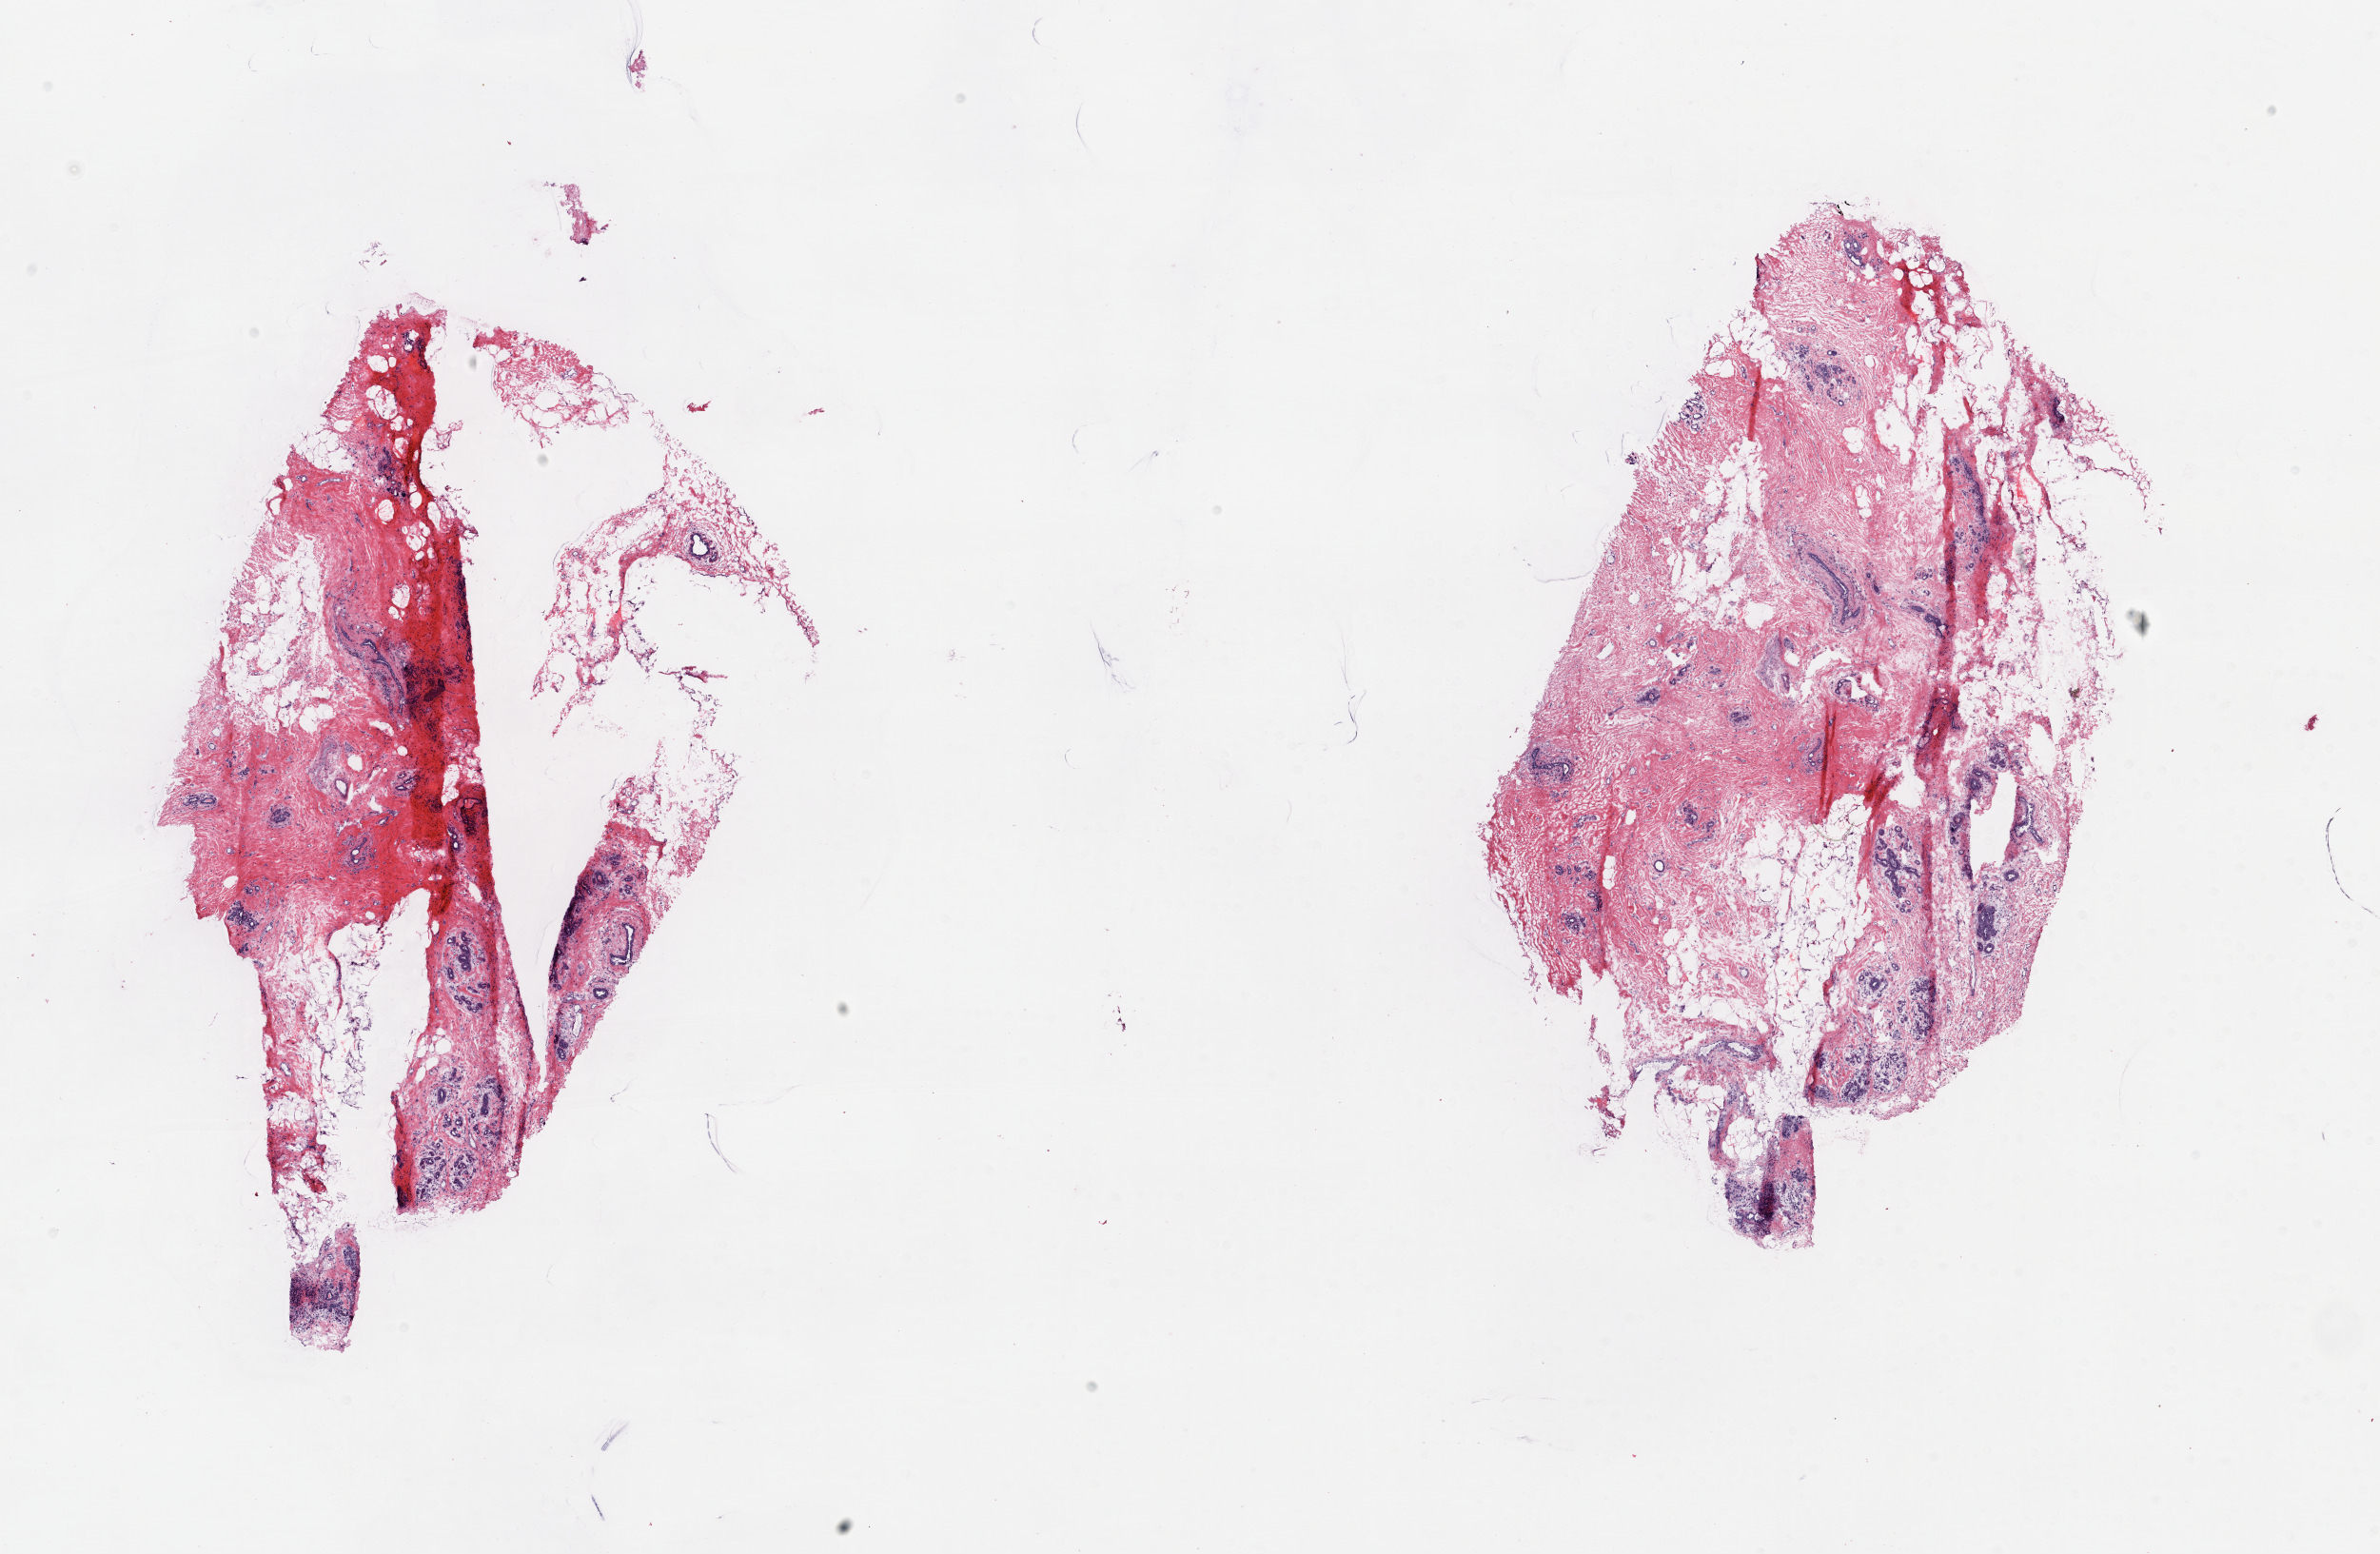
Whole-slide histology image, H&E — a low-resolution overview of the entire scanned area, about 19.8 x 13.0 mm (acquisition: 20x scan), frozen section, breast, solid tissue normal (non-tumour tissue) sample. Female patient; age at initial diagnosis 57 years. Pathologist review of this section (percent, as recorded): tumour cells 0%, normal cells 100%. Inflammatory infiltration, as recorded: lymphocyte infiltration 2%, monocyte infiltration 2%, neutrophil infiltration 0%.
This section: solid tissue normal sample (biorepository sample class). Patient diagnosis: Infiltrating duct carcinoma, NOS.